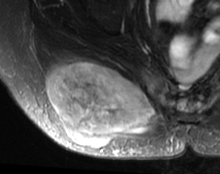
MRI of an extremity soft-tissue mass, one axial slice; position 26 of 63 along the scan axis; T2-weighted fat-saturated; MR volume resampled by the dataset authors to the PET/CT grid (not the native acquisition matrix); 3.27 mm slice thickness; 220 × 174 image matrix. Female patient. From the clinical record (not read from this slice): histological type: spindle cell suggestive of myxofibrosarcoma; grade: intermediate; site of the primary tumour: right buttock.
Structures marked on this image (expert contour drawn on MRI and transferred to this co-registered scan by the dataset authors):
- gross tumour volume (mass): bounding box <45,61,158,147> (left, top, right, bottom; pixels)